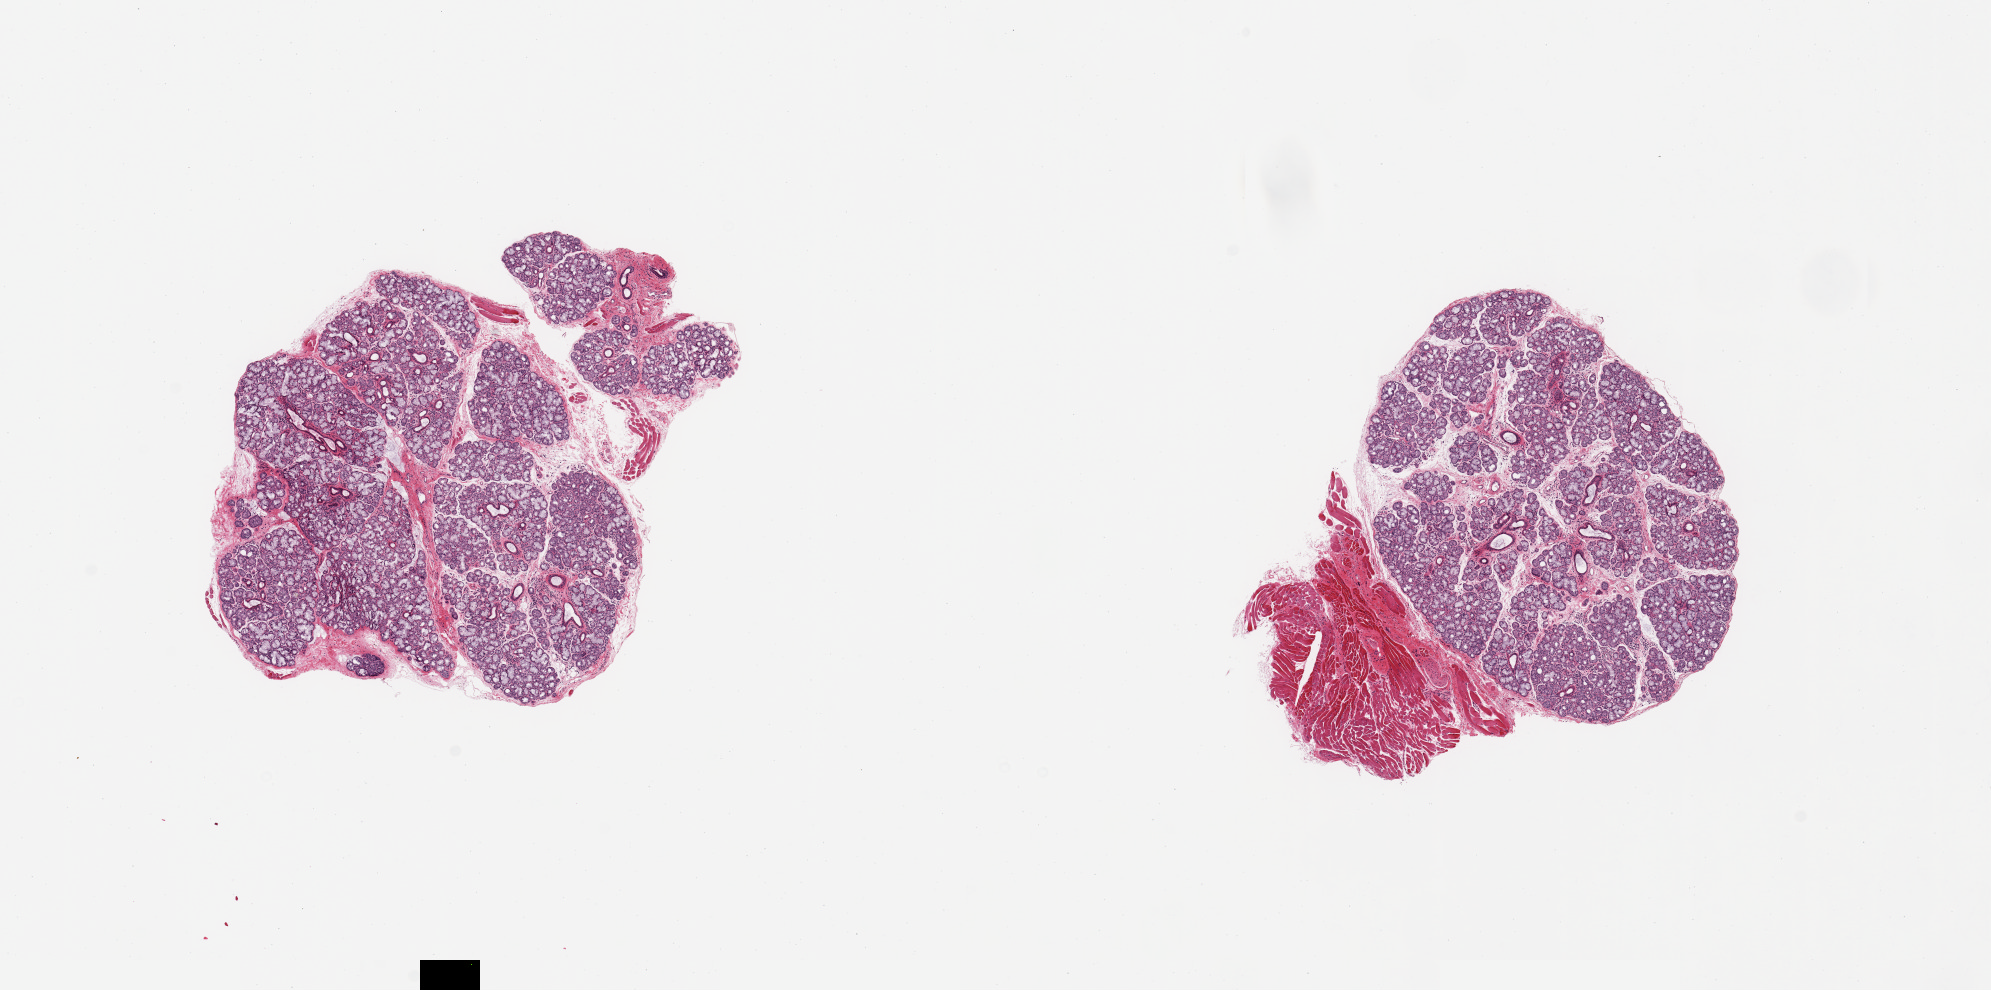
Whole-slide image, H&E stain — a low-resolution overview of the entire scanned area, about 15.8 x 7.8 mm (slide scanned at 20x), PAXgene-fixed, paraffin-embedded tissue, section of minor salivary gland (target tissue), tissue donor sample. Female donor.
Review note (as recorded): 2 pieces; excellent specimens, but 1 includes ~ 30% skeletal muscle, minimal chronic inflammation.